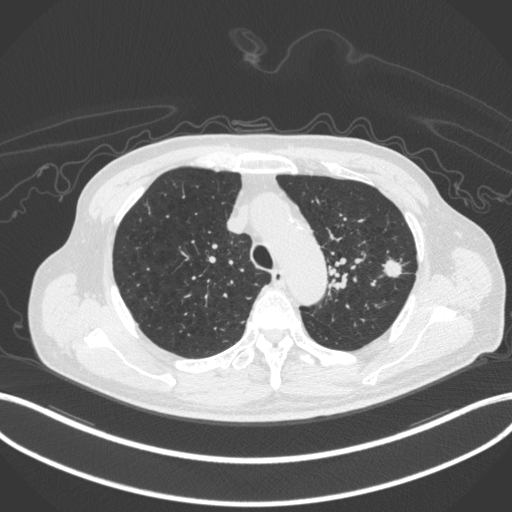
Chest CT, one axial slice. Position 336 of 420 along the scan axis. Lung window (W 1500 / L -600 HU). 1 mm slice thickness. 512 × 512 image matrix, field of view 400 × 400 mm. Patient: male, 77 years. Case-level facts recorded for this patient, not image findings: clinical TNM (as recorded): T3 N1 M0.
Outlined on this slice (rectangle marked by the reading radiologist):
- lung tumour (recorded histology: adenocarcinoma): bounding box <379,256,404,281> (left, top, right, bottom; pixels)